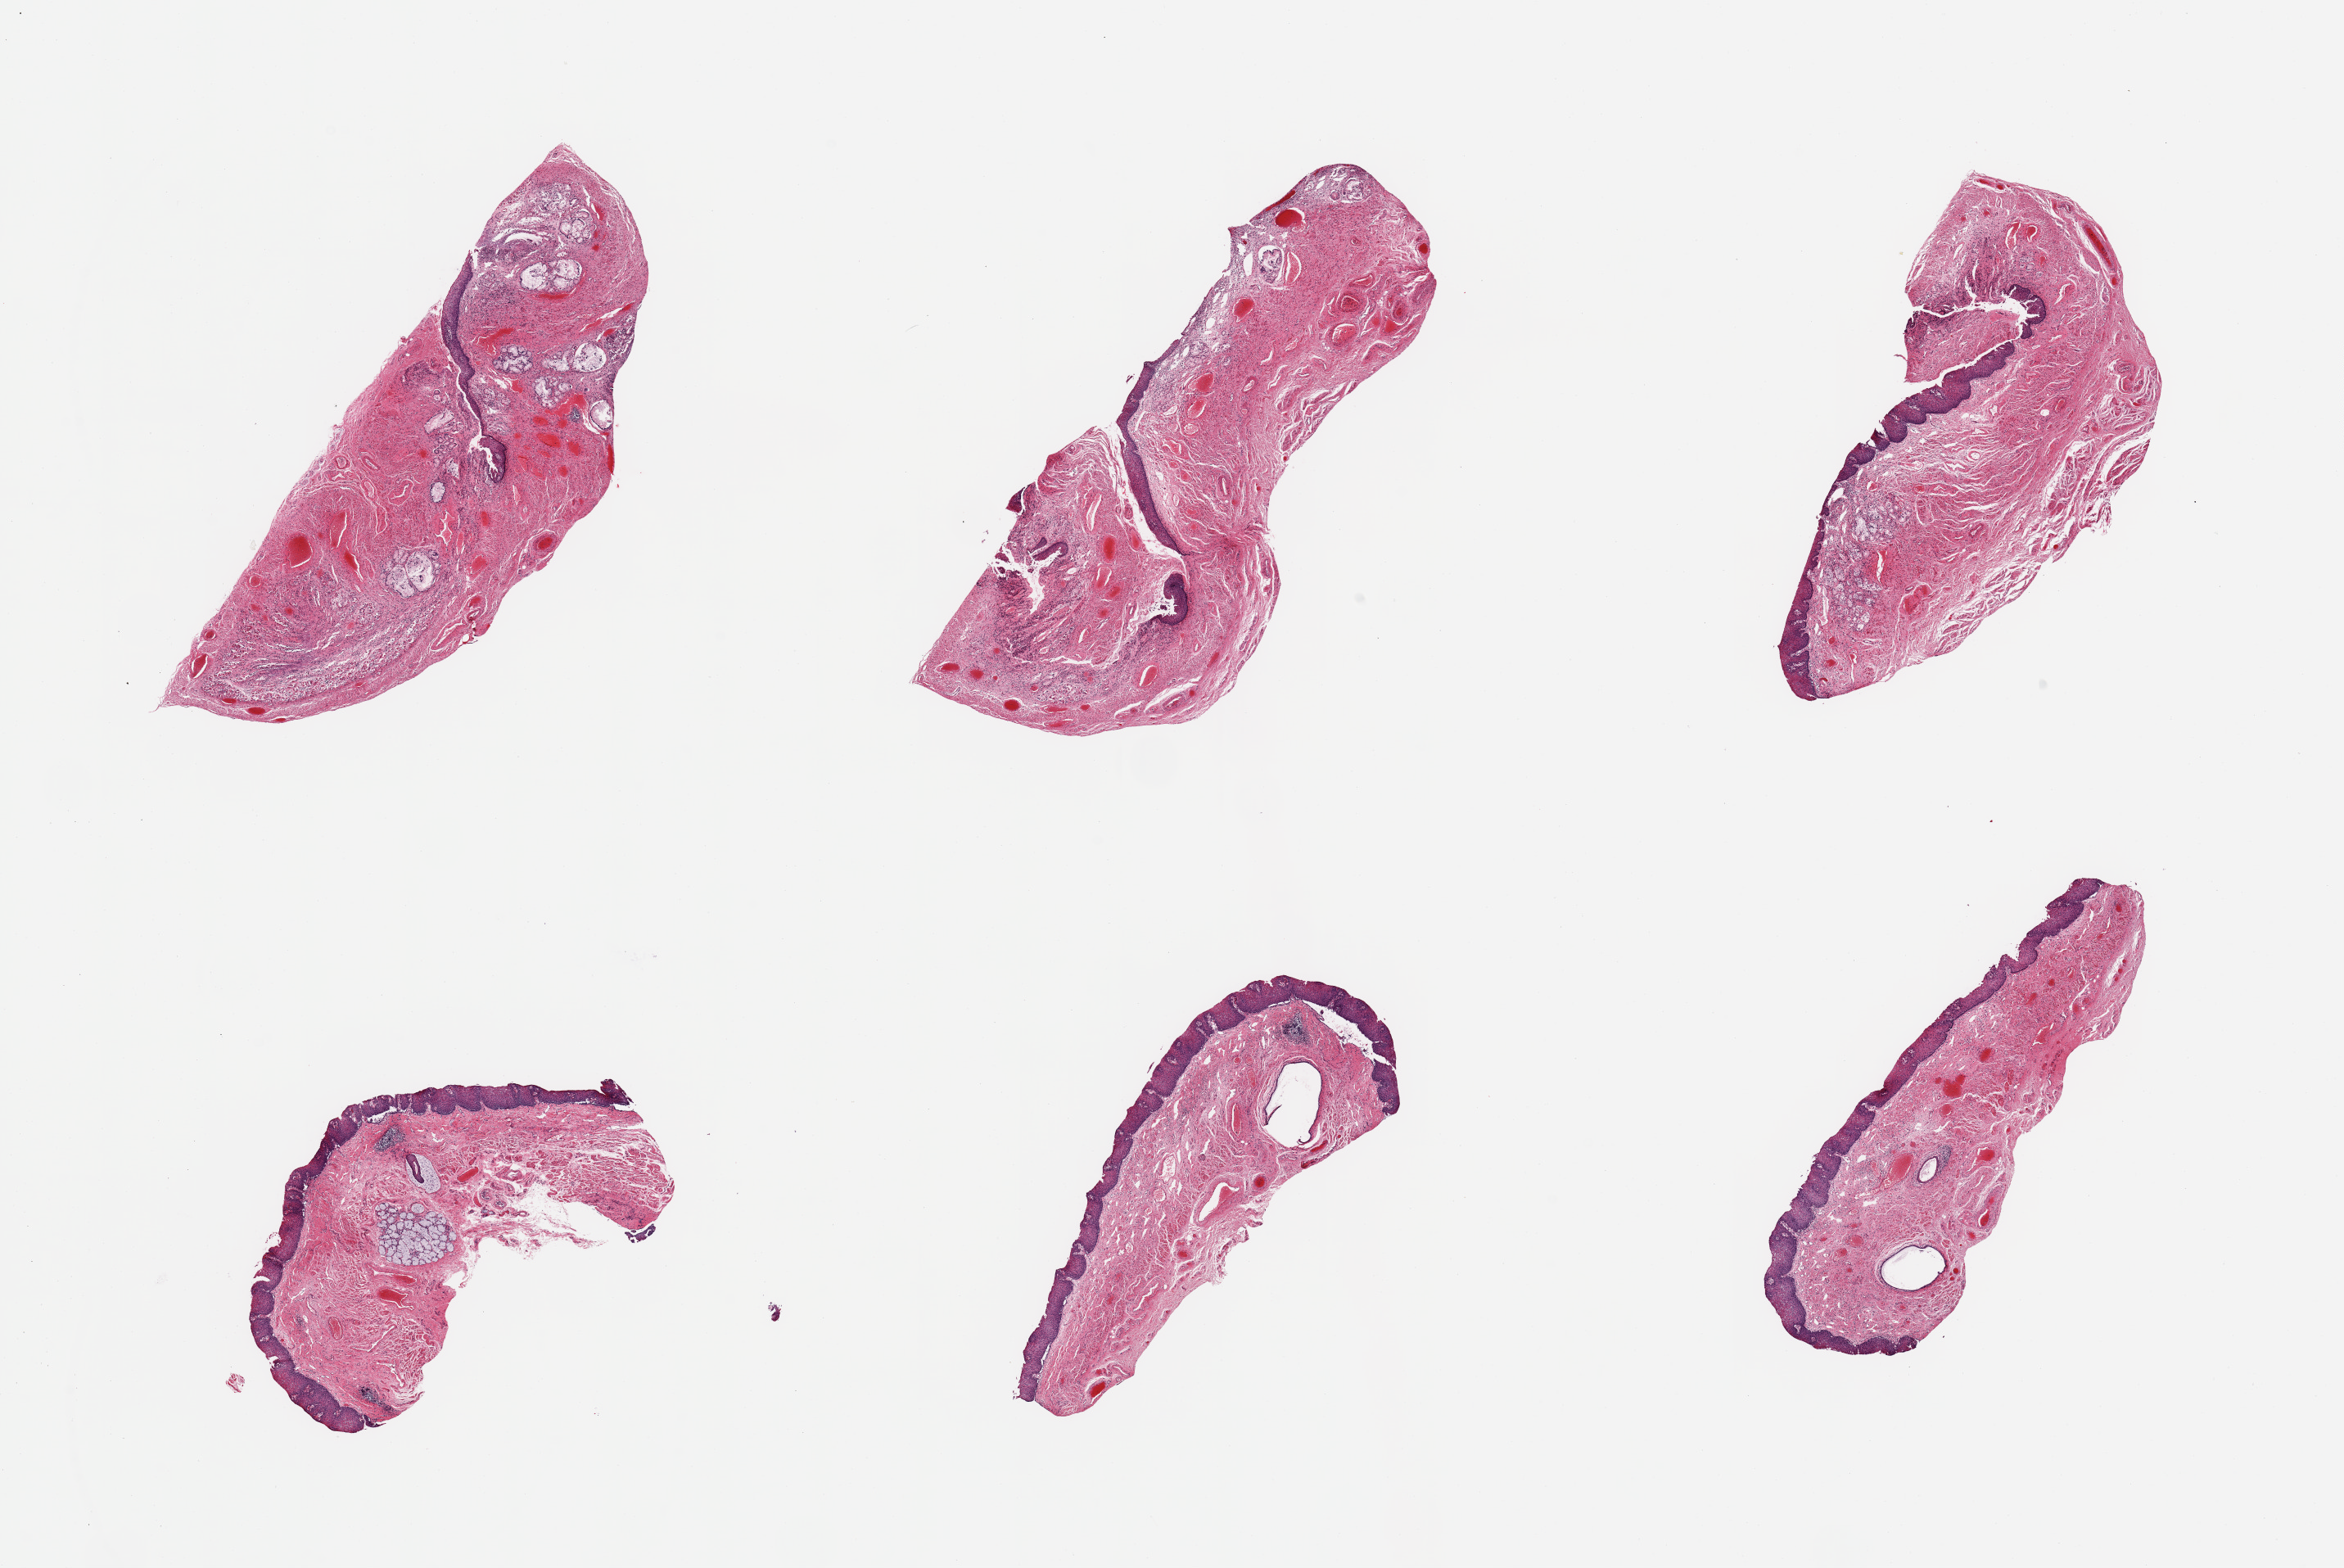
H&E whole-slide image — shown as a low-resolution overview of the whole scanned area (about 22.6 x 15.1 mm, from a 20x scan), PAXgene-fixed, paraffin-embedded tissue, target tissue: gastroesophageal junction, donor tissue sample. Male donor.
Reviewer comment on this tissue sample: 6 pieces; not muscularis, mucosa of GE junction with few dilated glands.